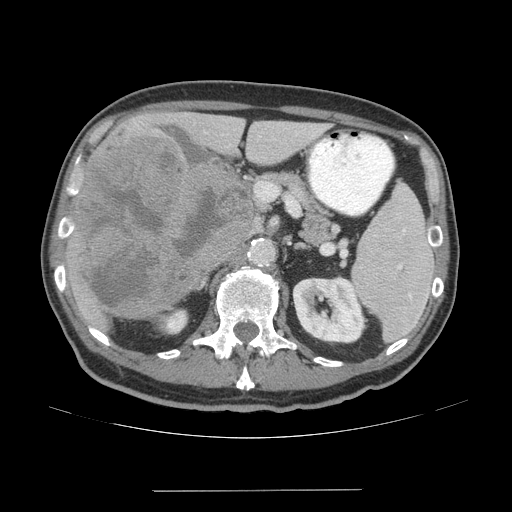
Contrast-enhanced abdominal CT (liver protocol), one axial slice; position 27 of 77 along the scan axis; reconstruction kernel STANDARD; 140 kVp; soft-tissue window (W 400 / L 40 HU); 2.5 mm slice thickness; 512 × 512 image matrix, field of view 400 × 400 mm. From the clinical record (not read from this slice): diagnosis: hepatocellular carcinoma (patient treated with transarterial chemoembolisation; whether this scan precedes or follows treatment is not stated here); TNM stage (as recorded): Stage-IVA; Child-Pugh class: A; tumour differentiation: well differentiated.
Outlined on this slice (semi-automatically segmented with operator editing):
- liver parenchyma outside the tumour (the mass and vessels are separate outlines, so this box may not span the whole liver): box from (x=66, y=112) to (x=323, y=324) px
- mass: (x=74, y=138)–(x=255, y=320)